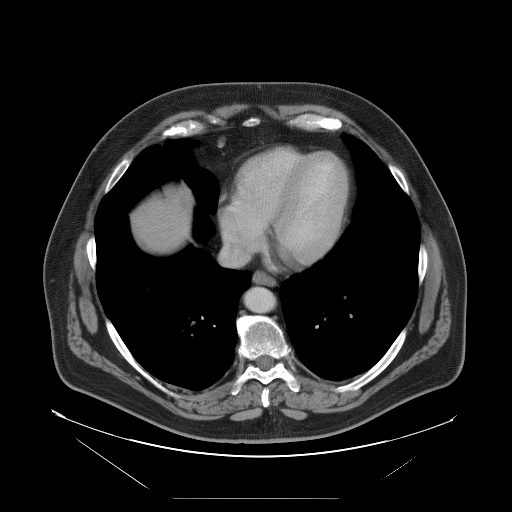
Contrast-enhanced abdominal CT, one axial slice; slice 98 of 114 in the series (ordered by position); 120 kVp; intravenous contrast given; soft-tissue window (W 400 / L 40 HU); 512 × 512 image matrix, field of view 500 × 500 mm. Male patient, age 61 years. Case-level facts recorded for this patient, not image findings: diagnosis: colorectal cancer liver metastases, imaged before liver resection; multiple liver metastases: no; largest metastasis: 6.5 cm; disease in both lobes: yes.
Outlined on this slice (expert manual segmentation):
- hepatic veins: bounding box (x1, y1, x2, y2) in pixels: (221, 214, 268, 266)
- liver: (133, 198, 189, 252)